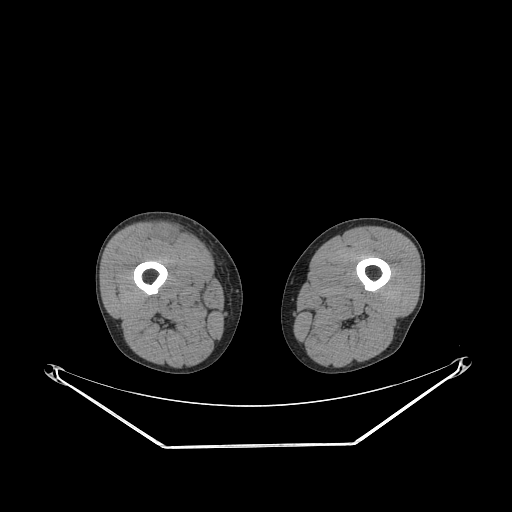
CT of an extremity soft-tissue mass (from a PET/CT study), one axial slice. Slice 235 of 311 in the series (ordered by position). 140 kVp. Soft-tissue window (W 400 / L 40 HU). 3.75 mm slice thickness. 512 × 512 image matrix. Male patient. Case-level facts recorded for this patient, not image findings: histological type: pleiomorphic leiomyosarcoma; grade: intermediate; site of the primary tumour: right thigh.
Outlined on this slice (expert contour drawn on MRI and transferred to this co-registered scan by the dataset authors):
- gross tumour volume including surrounding oedema: box from (x=155, y=226) to (x=182, y=243) px